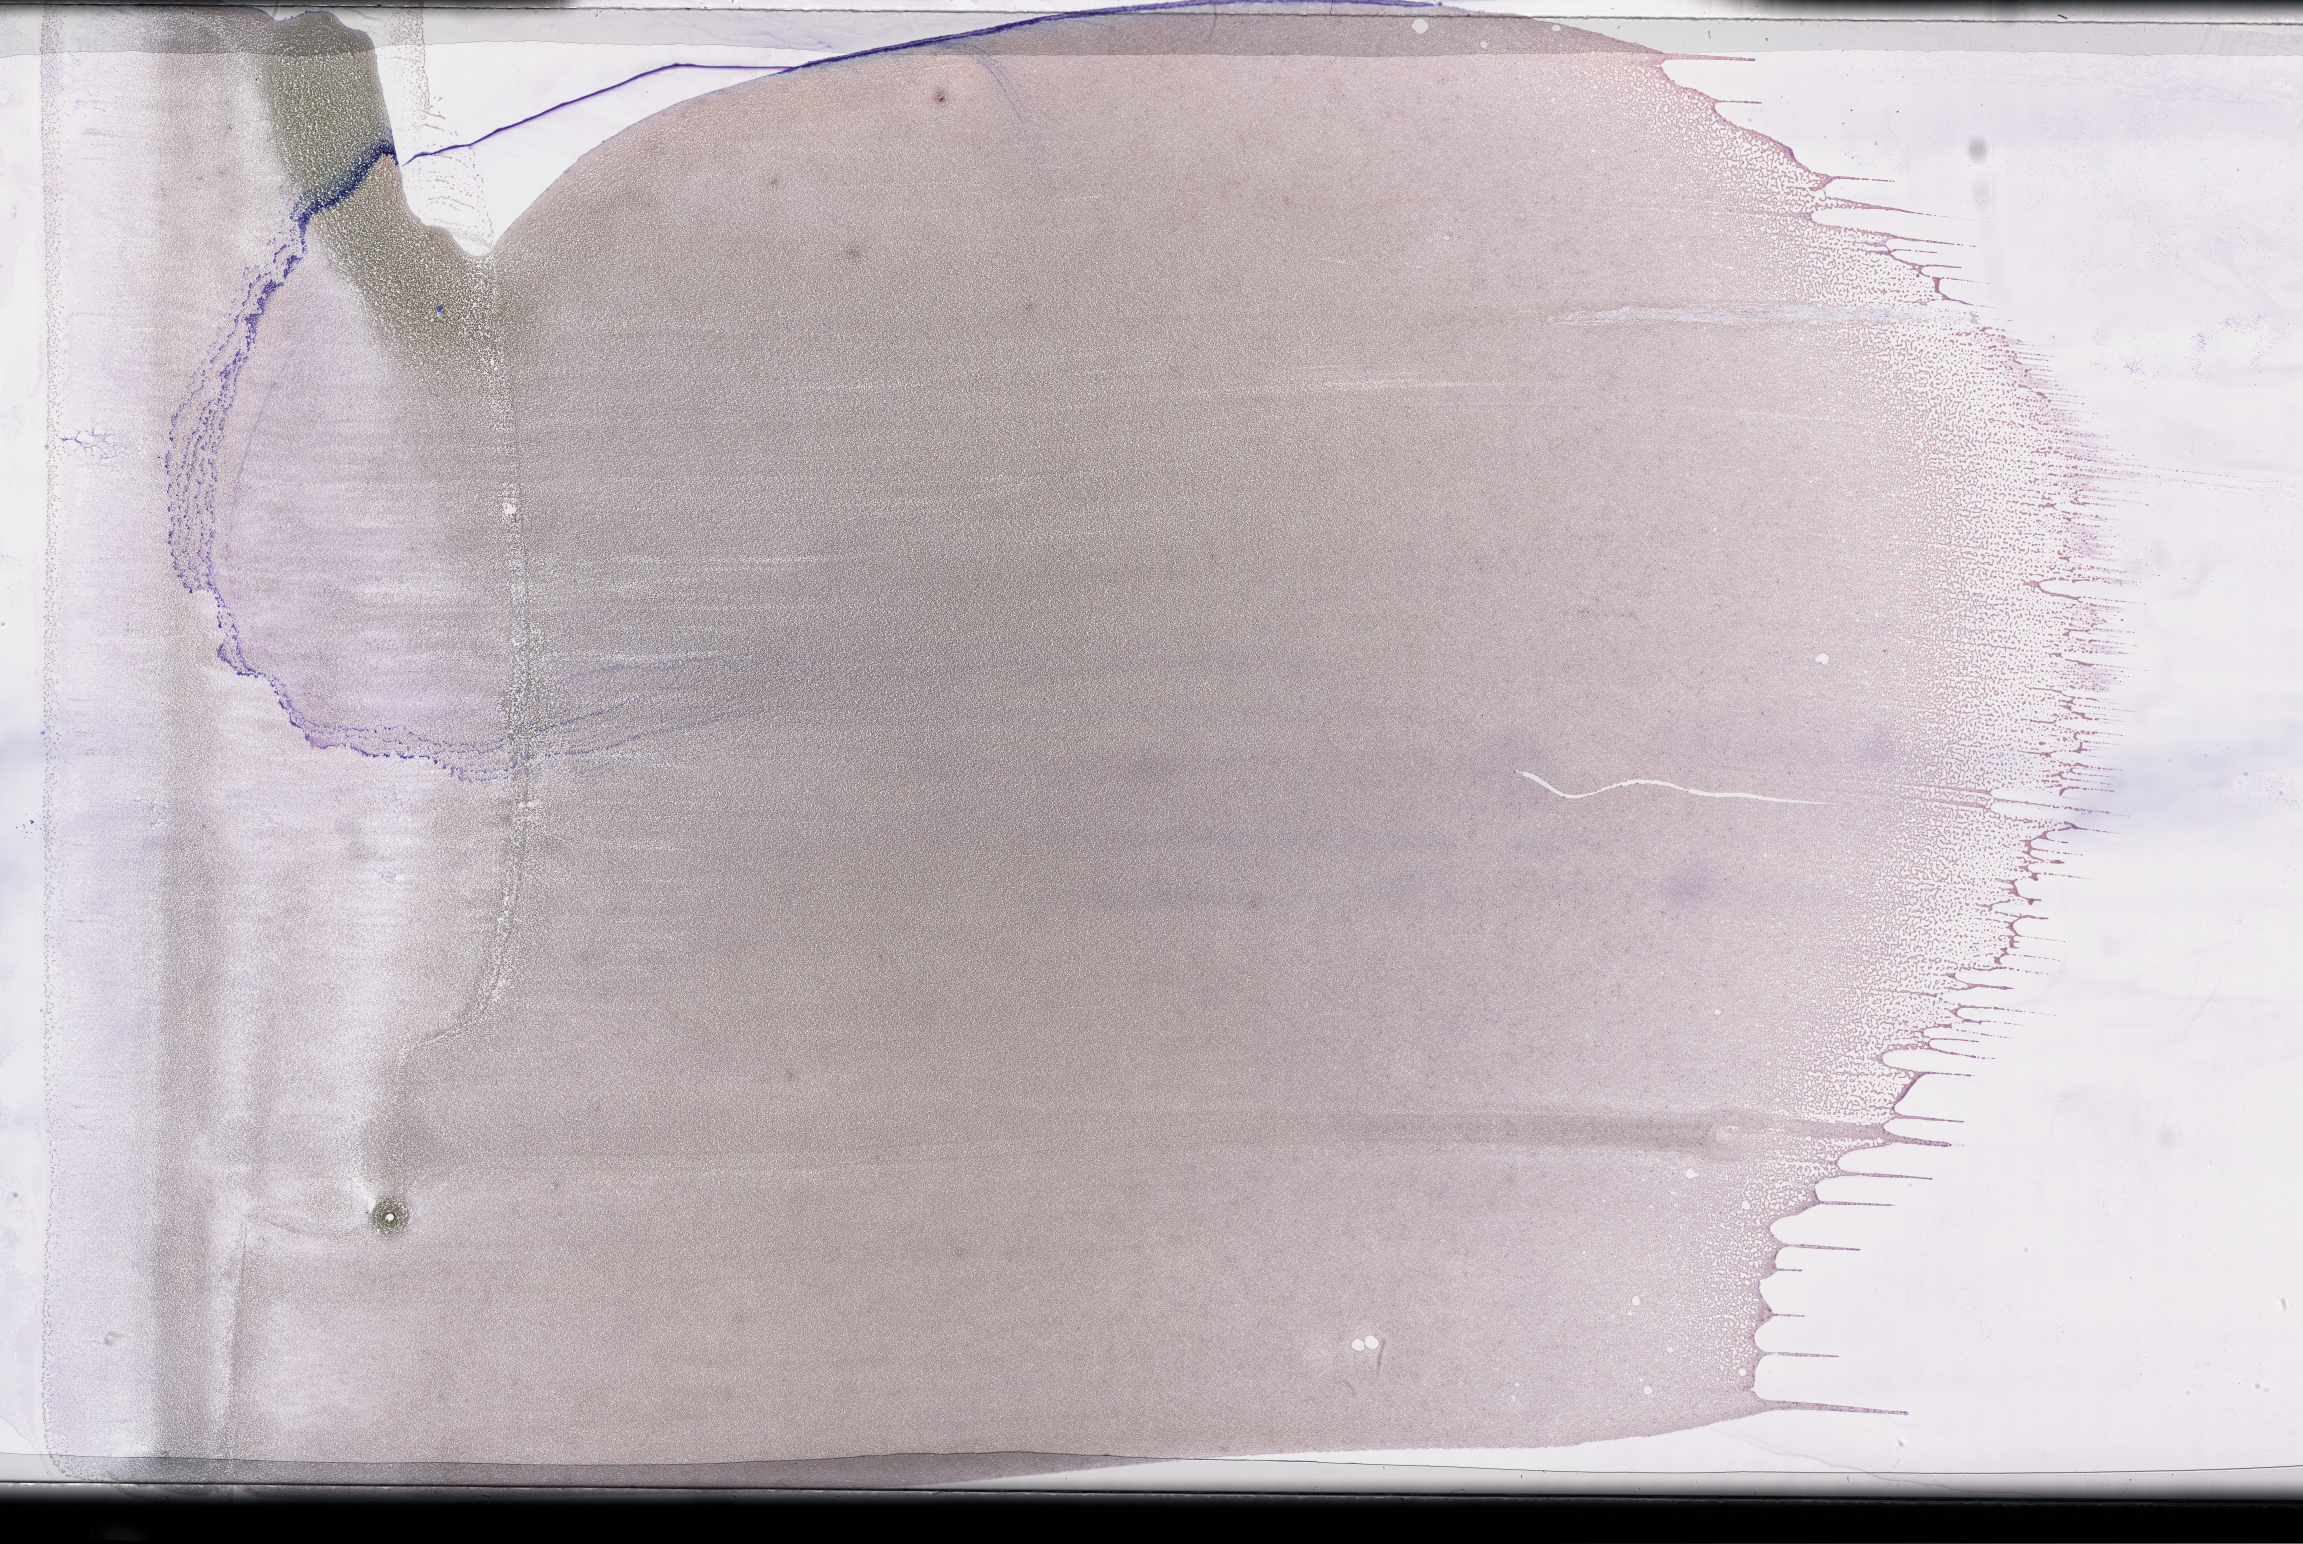
Whole-slide image of a whole blood smear, Wright-Giemsa stain, whole scanned area (about 37.2 x 24.9 mm) shown as a low-resolution overview. Male patient.
Patient diagnosis: Plasma Cell Myeloma.